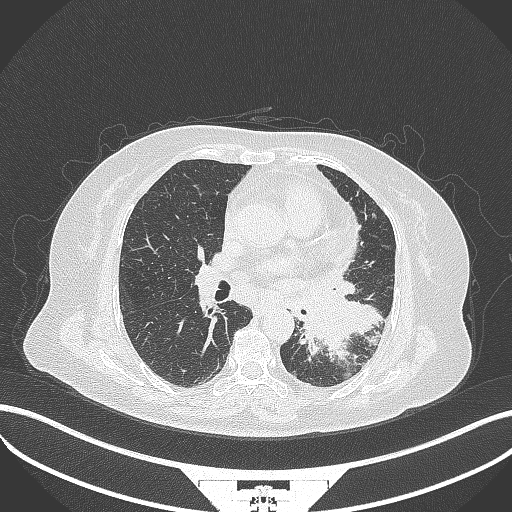
Chest CT, one axial slice. Position 179 of 322 along the scan axis. Lung window (W 1500 / L -600 HU). 1 mm slice thickness. 512 × 512 image matrix. Female patient, age 69 years. From the clinical record (not read from this slice): clinical TNM (as recorded): T2b N3 M1.
Structures marked on this image (rectangle marked by the reading radiologist):
- lung tumour (recorded histology: adenocarcinoma): bounding box <299,287,385,369> (left, top, right, bottom; pixels)